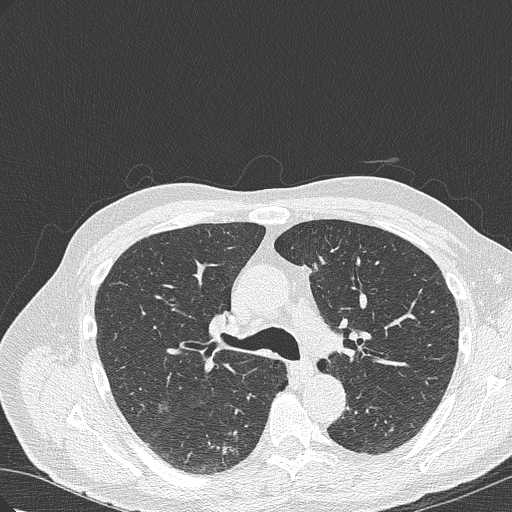
Axial slice from a low-dose chest CT screening exam. Baseline screening round. Lung window (W 1500 / L -600 HU). 1 mm slice thickness. Lung (sharp) reconstruction kernel (B50f). 120 kVp. 512 × 512 image matrix, field of view 350 × 350 mm. Male, age 70 years at enrolment.
Expert-annotated lung lesion, bounding box [x1, y1, x2, y2] px = [201, 418, 266, 466]. The screening reader recorded 4 non-calcified nodules or masses ≥4 mm on this exam (right lower lobe, right lower lobe, right upper lobe, right lower lobe); which of them this box marks is not recorded. Official screen result: positive, change unspecified: nodule(s) >= 4 mm or enlarging nodule(s), mass(es), or other non-specific abnormalities suspicious for lung cancer. Participant outcome: lung cancer diagnosed 978 days after this screen — bronchiolo-alveolar adenocarcinoma, NOS, right lower lobe, poorly differentiated (G3), stage IB (AJCC 6th edition), 30 mm at pathology.